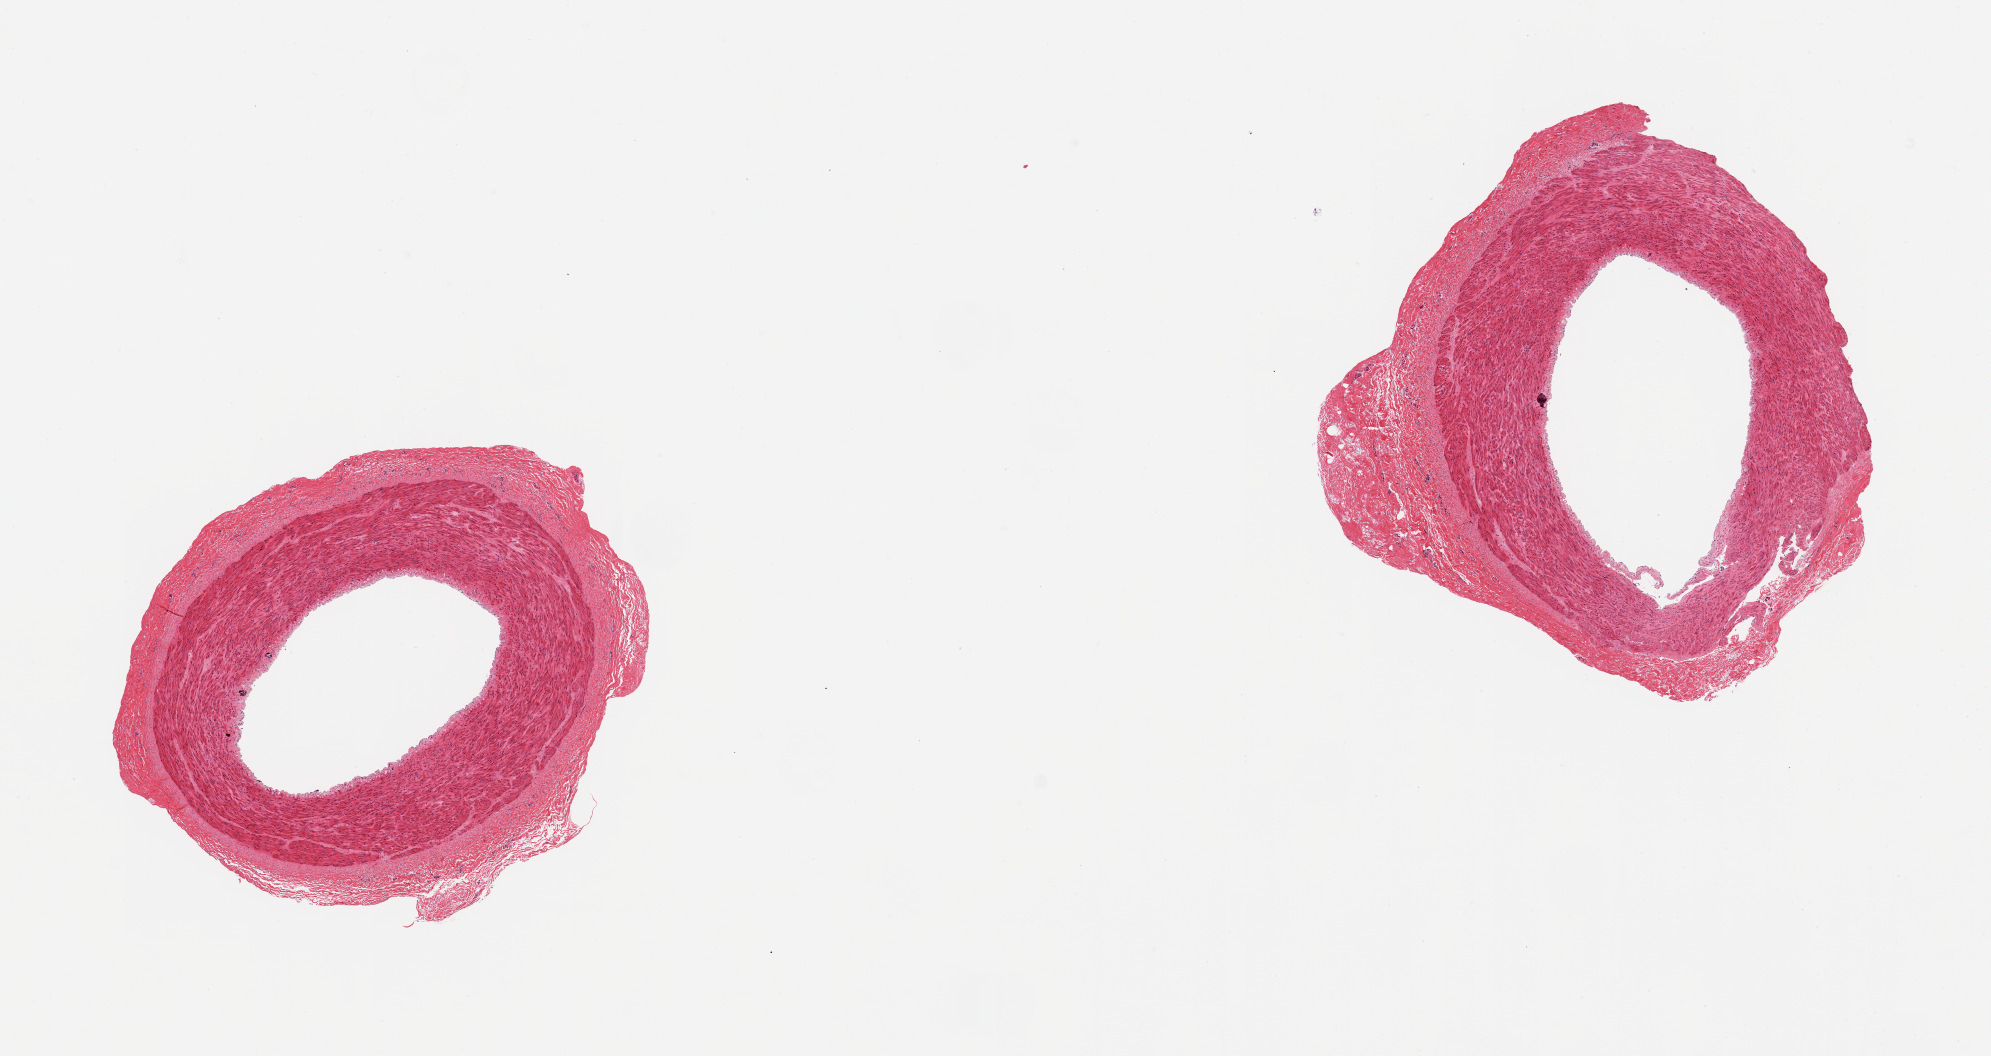
Digitized haematoxylin and eosin-stained section, shown as a low-resolution overview of the whole scanned area (about 15.8 x 8.4 mm); PAXgene-fixed, paraffin-embedded tissue; target tissue: tibial artery; tissue donor sample. Donor sex: male.
Review note (as recorded): 2 pieces; several minute (56um) subintimal calcific deposits; otherwise no plaques; well dissected.